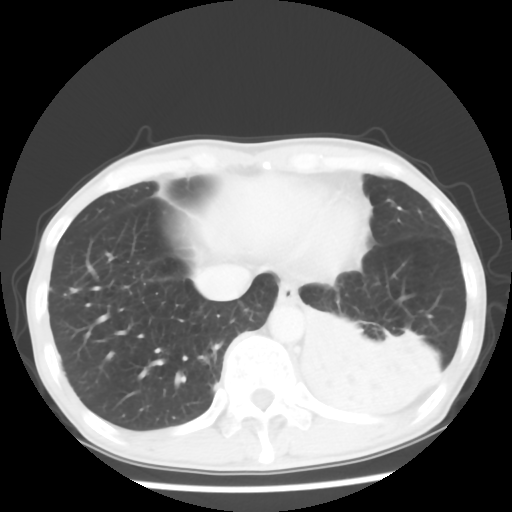
Chest CT, one axial slice; position 13 of 64 along the scan axis; reconstruction kernel STANDARD; lung window (W 1500 / L -600 HU); 5 mm slice thickness; 512 × 512 image matrix, field of view 313 × 313 mm. Patient: male, 68 years. Case-level facts recorded for this patient, not image findings: clinical TNM (as recorded): T4 N0 M0.
Structures marked on this image (bounding box drawn by a radiologist):
- lung tumour (recorded histology: squamous cell carcinoma): bounding box <291,301,455,433> (left, top, right, bottom; pixels)